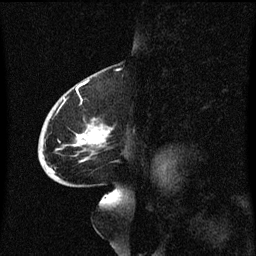
Breast MRI (dynamic contrast-enhanced), one sagittal slice; dynamic contrast-enhanced series, image 2 of 3 at this slice position (ordered by acquisition); 1.5 T; TE 4.2 ms, TR 8.4 ms; 256 × 256 image matrix, field of view 200 × 200 mm. Female patient, age 68 years. From the clinical record (not read from this slice): setting: breast cancer imaged before/during neoadjuvant chemotherapy; receptor status: triple-negative.
Annotated regions visible in this slice (semi-automatically segmented with operator editing):
- analysis volume of interest (the breast-tissue region the enhancement analysis was run in; not a lesion): bounding box (x1, y1, x2, y2) in pixels: (39, 94, 115, 173)
- tumour enhancement mask (voxels above the 70 % enhancement threshold inside the analysis volume of interest): (41, 122, 111, 173)